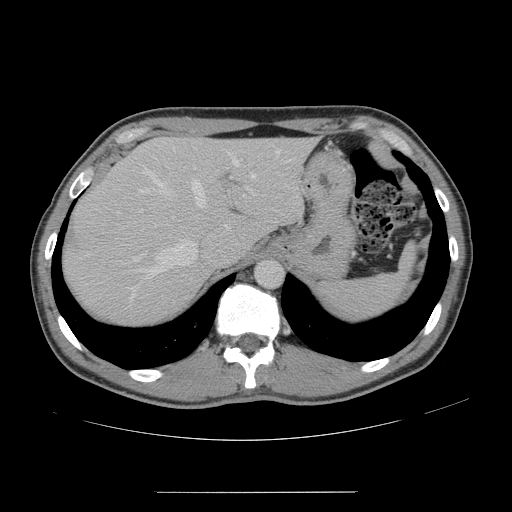
Contrast-enhanced abdominal CT, one axial slice; position 117 of 178 along the scan axis; intravenous contrast given; soft-tissue window (W 400 / L 40 HU); 2.5 mm slice thickness; 512 × 512 image matrix, field of view 401 × 401 mm. Male patient, age 53 years. Case-level facts recorded for this patient, not image findings: diagnosis: colorectal cancer liver metastases, imaged before liver resection; multiple liver metastases: yes.
Structures marked on this image (manually delineated by an expert):
- hepatic veins: box from (x=127, y=150) to (x=280, y=299) px
- liver: (x=64, y=138)–(x=311, y=323)
- planned liver remnant (the part of the liver to remain after resection): (x=147, y=138)–(x=311, y=246)
- portal vein (with intrahepatic branches): (x=139, y=187)–(x=255, y=213)